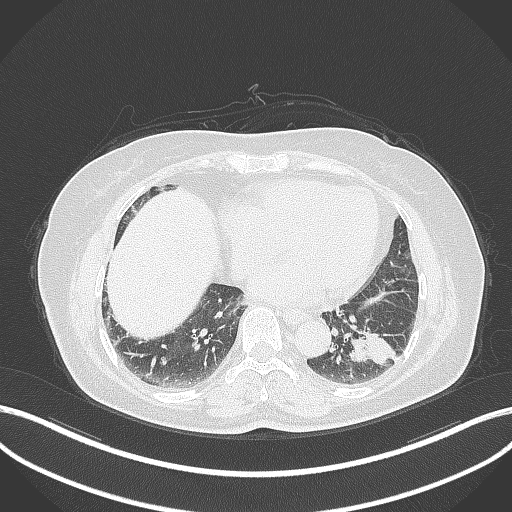
Chest CT, one axial slice; slice 133 of 311 in the series (ordered by position); reconstruction kernel B70f; 120 kVp; lung window (W 1500 / L -600 HU); 512 × 512 image matrix, field of view 400 × 400 mm. Female patient, age 59 years. From the clinical record (not read from this slice): clinical TNM (as recorded): T2a N0 M0; histopathological grade: G2-3.
Annotated regions visible in this slice (bounding box drawn by a radiologist):
- lung tumour (recorded histology: adenocarcinoma): bounding box [x1, y1, x2, y2] px = [345, 324, 401, 368]